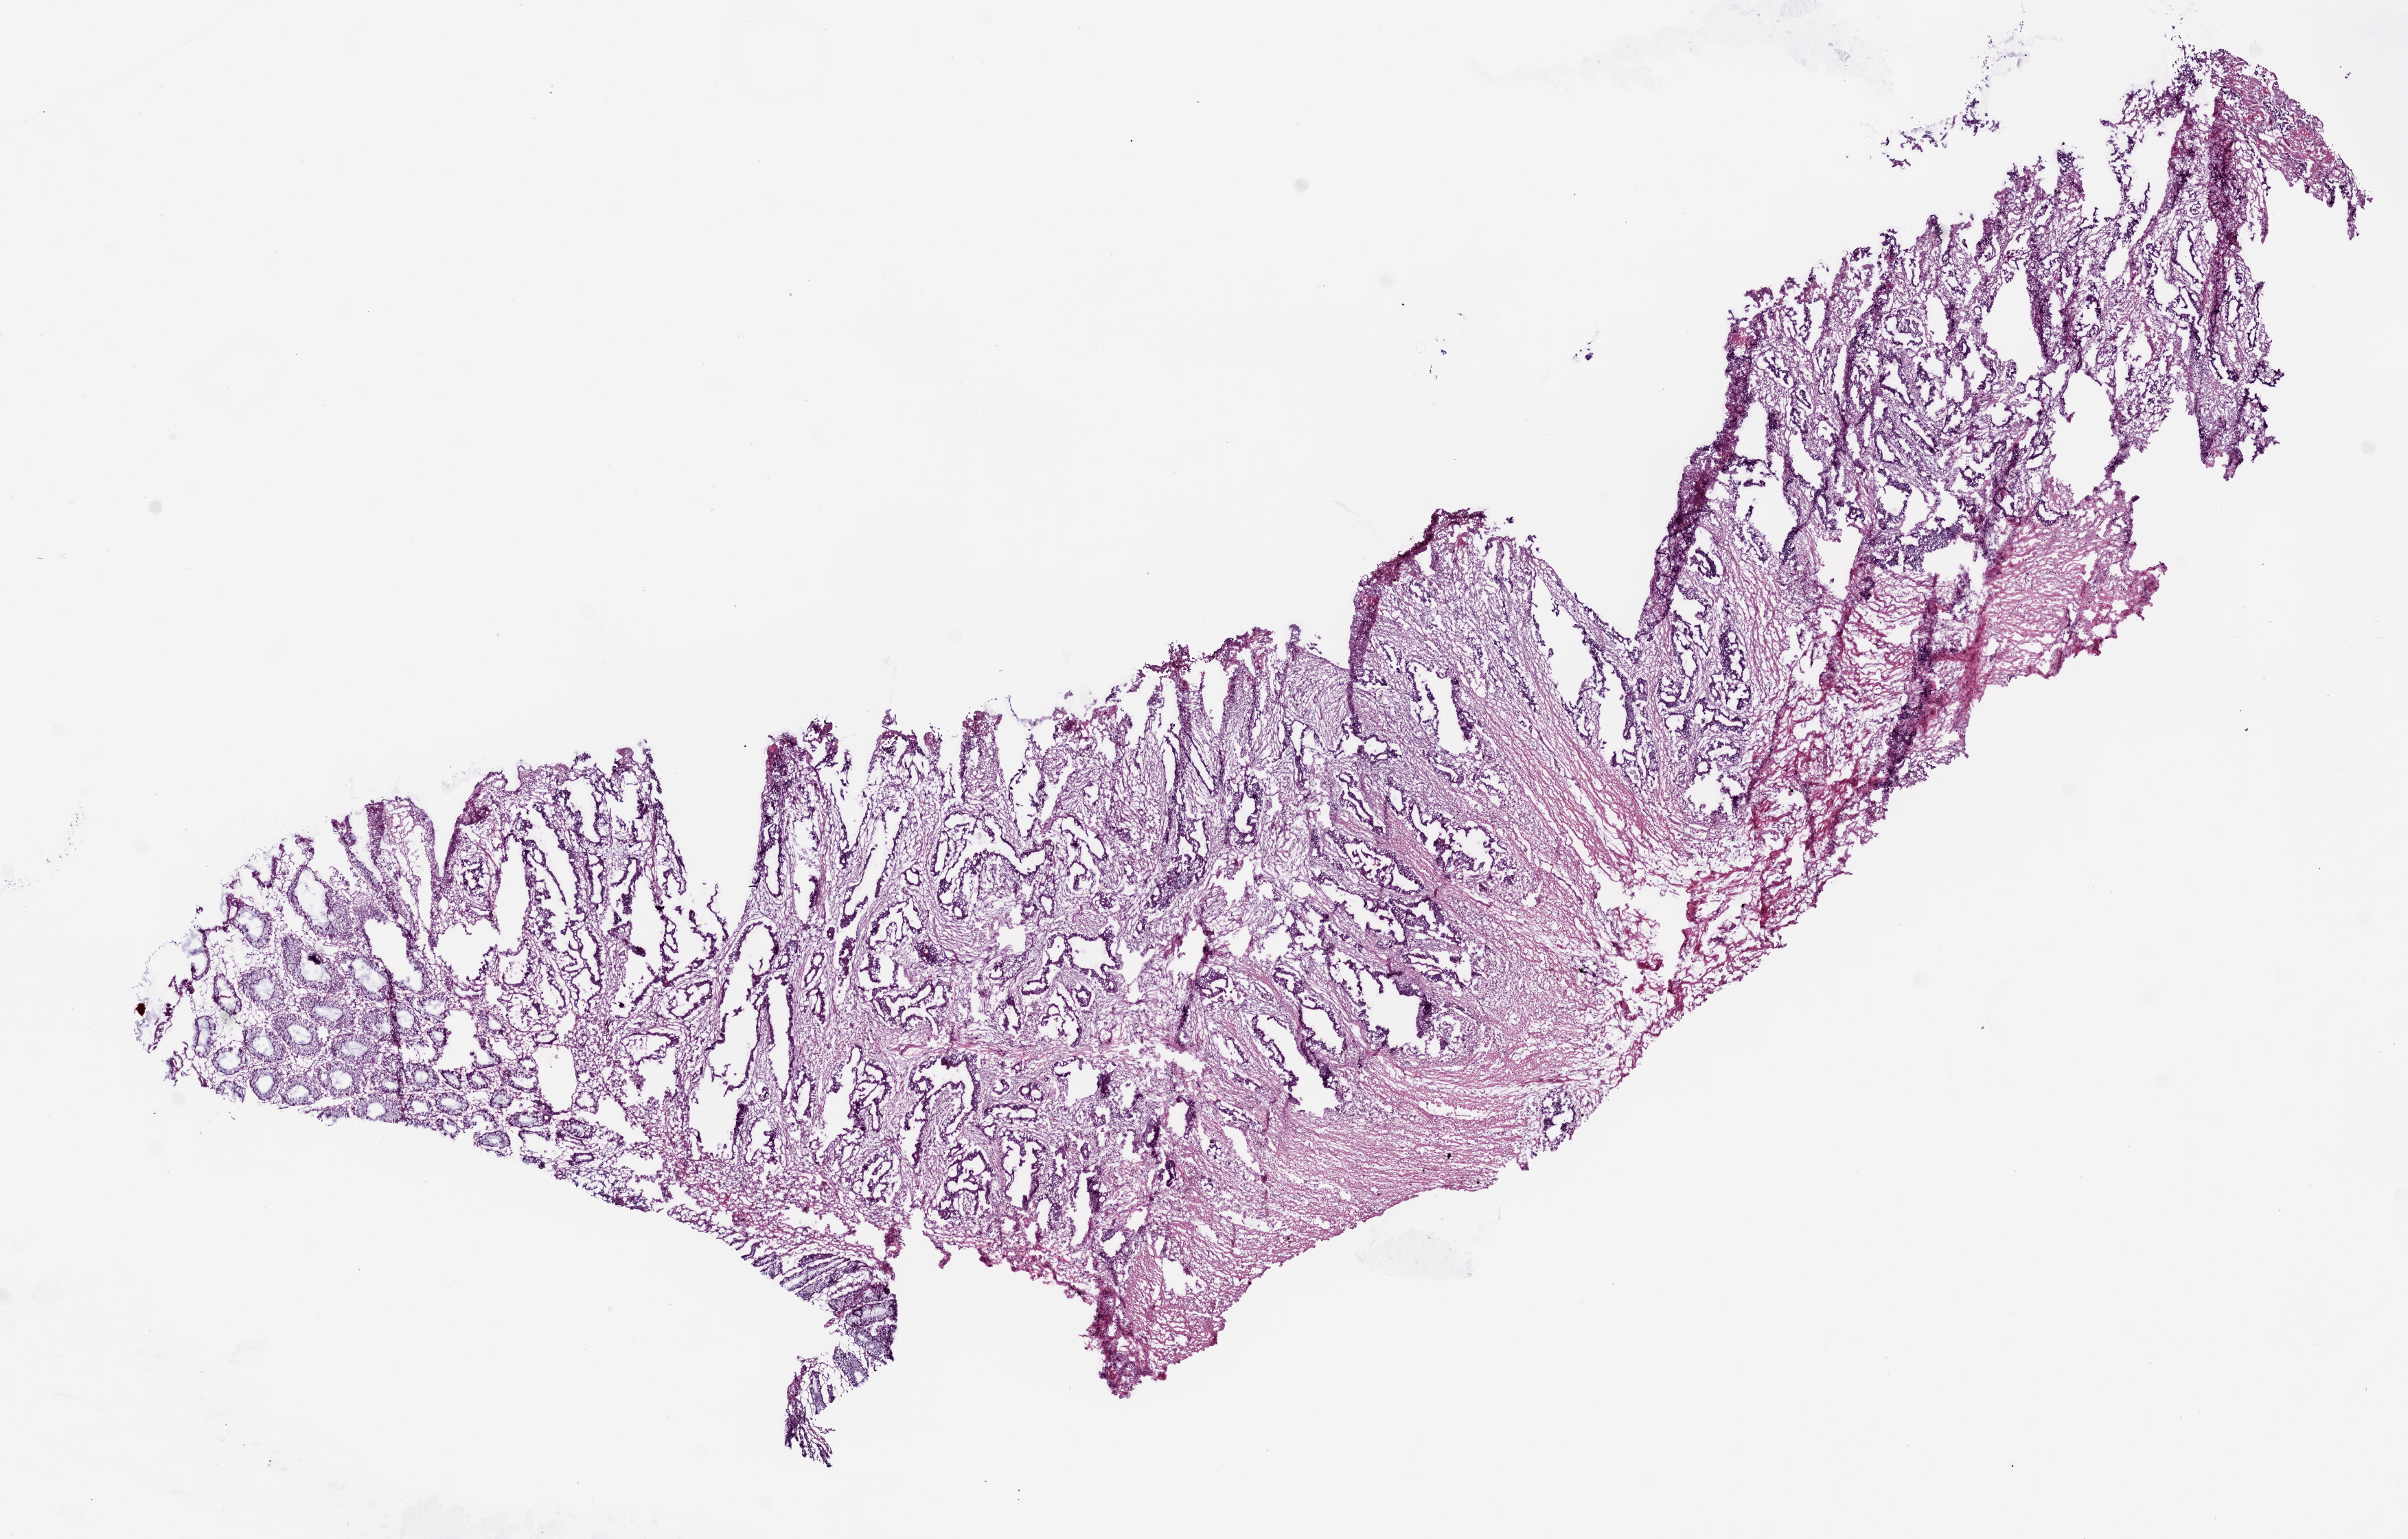
Digitized Hematoxylin and eosin (H&E) stained tissue section (whole slide), a low-resolution overview of the entire scanned area, about 14.1 x 9.0 mm (from a 5x scan). Frozen section from the bottom of the tissue portion. Colon, primary tumour sample. Male patient; age at initial diagnosis 43 years. Pathologist review of this section (percent, as recorded): tumour cells 57%, tumour nuclei 75%, normal cells 8%, stromal cells 35%, necrosis 0%.
Lymph nodes positive (case pathology): 0 of 12 examined. AJCC pathologic stage: II (5th edition). Histologic diagnosis: Adenocarcinoma, NOS.